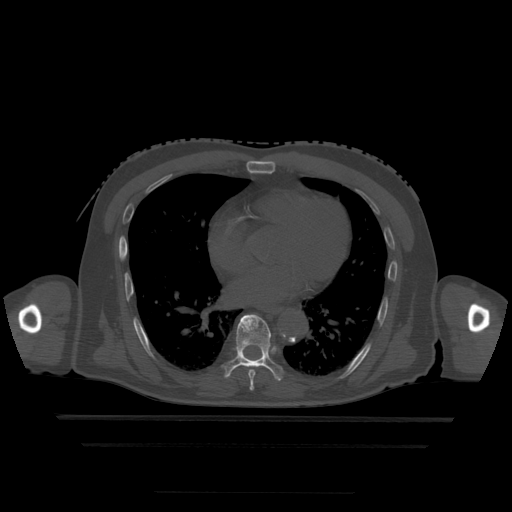
CT including the spine, one axial slice; bone window (W 1800 / L 400 HU); 1.25 mm slice thickness; 512 × 512 image matrix, field of view 436 × 436 mm. Patient age 68 years. From the clinical record (not read from this slice): primary cancer: urothelial.
Structures marked on this image (semi-automatically segmented with operator editing):
- T7 vertebra: box from (x=249, y=370) to (x=255, y=390) px
- T8 vertebra: (x=223, y=315)–(x=284, y=382)